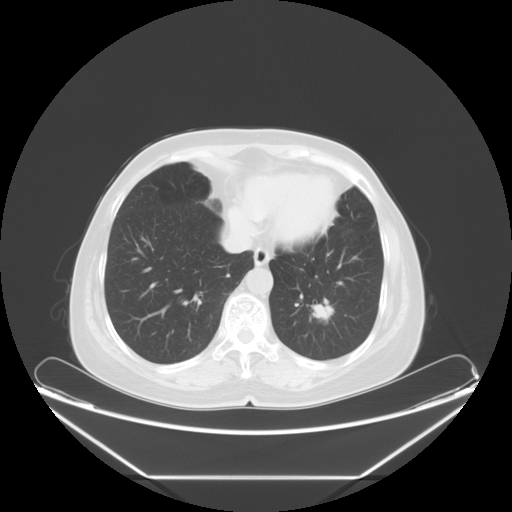
Chest CT, one axial slice. Position 19 of 61 along the scan axis. 120 kVp. Lung window (W 1500 / L -600 HU). 512 × 512 image matrix, field of view 451 × 451 mm. Female patient, age 63 years. From the clinical record (not read from this slice): clinical TNM (as recorded): T1c N0 M0; histopathological grade: G2-3.
Annotated regions visible in this slice (rectangle marked by the reading radiologist):
- lung tumour (recorded histology: adenocarcinoma): bounding box [x1, y1, x2, y2] px = [308, 295, 335, 325]